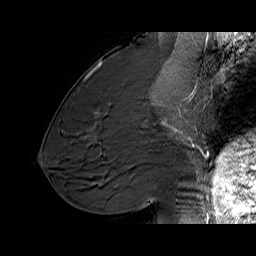
Breast MRI (dynamic contrast-enhanced), one sagittal slice; dynamic contrast-enhanced series, time point 2 of 6 at this slice position (early post-contrast); 1.5 T; TE 6.1 ms, TR 32.9 ms; 4 mm slice thickness; 256 × 256 image matrix, field of view 220 × 220 mm. Female patient. From the clinical record (not read from this slice): setting: breast cancer imaged before/during neoadjuvant chemotherapy; receptor status: HER2-positive.
Annotated regions visible in this slice (semi-automatically segmented with operator editing):
- analysis volume of interest (the breast-tissue region the enhancement analysis was run in; not a lesion): bounding box [x1, y1, x2, y2] px = [127, 95, 194, 165]
- tumour enhancement mask (voxels above the 100 % enhancement threshold inside the analysis volume of interest): [161, 95, 192, 140]